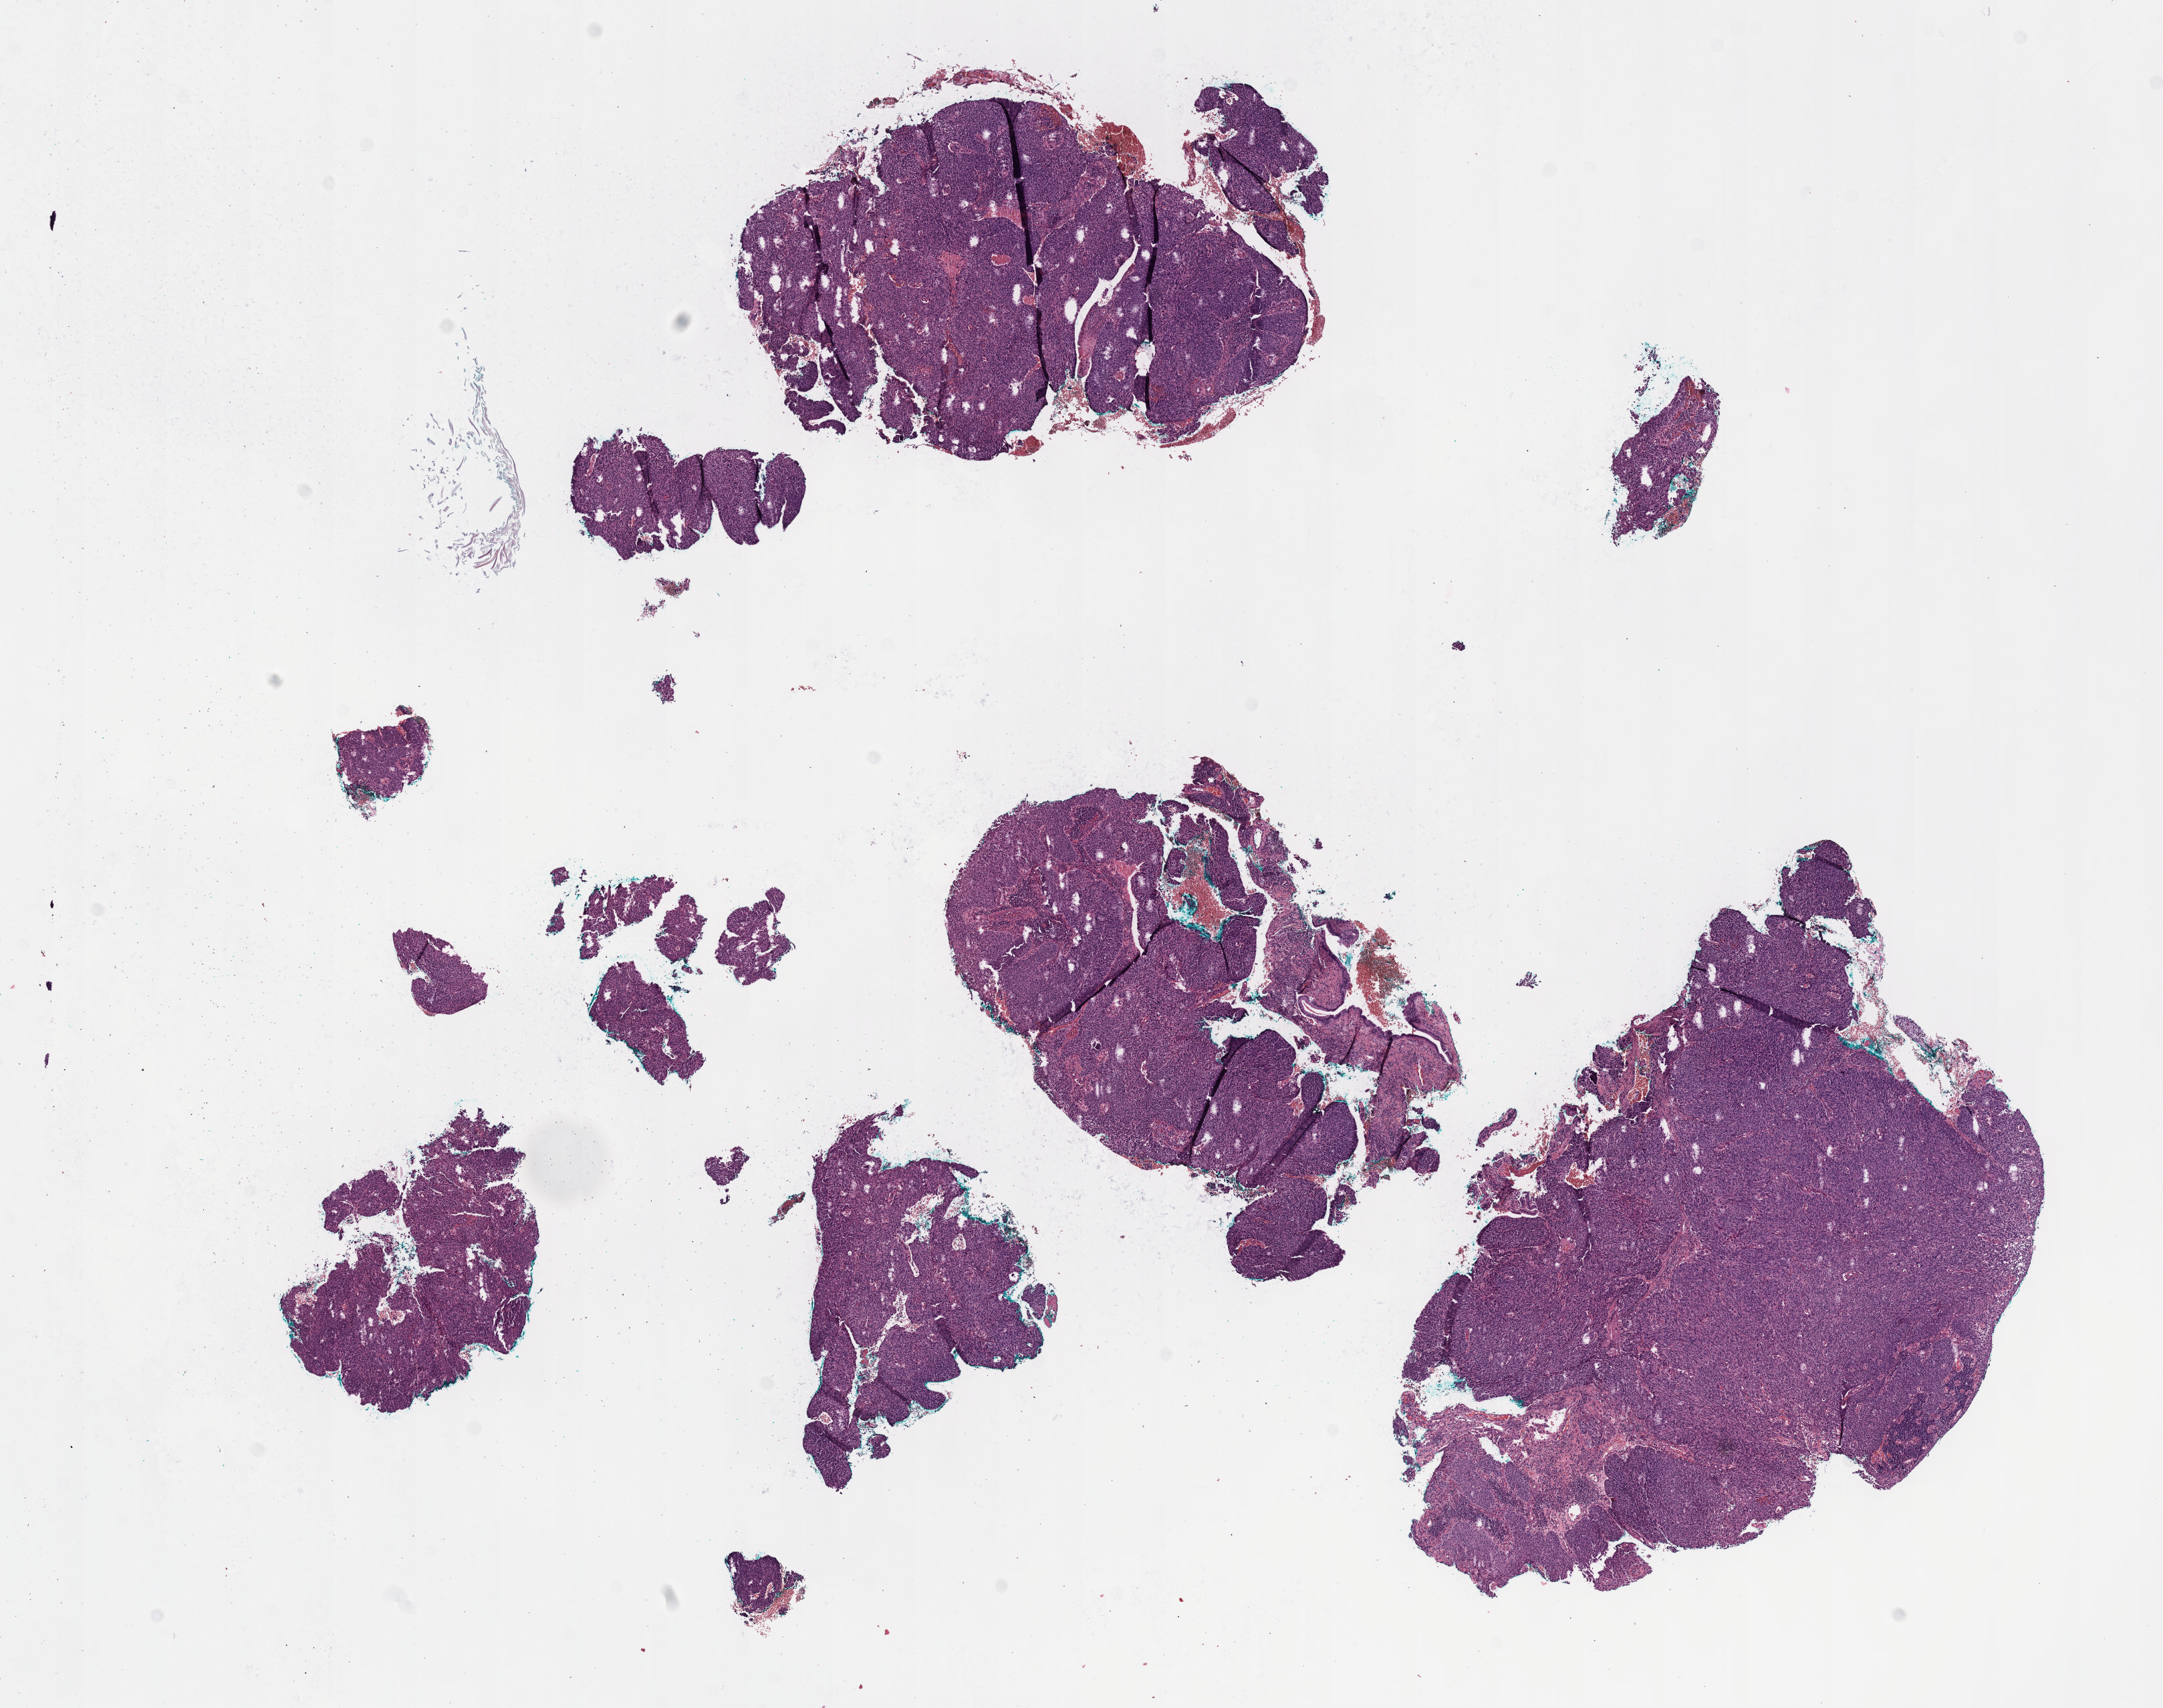
Whole-slide histology image, H&E, low-resolution overview of the scanned area, about 13.1 x 10.3 mm (from a 40x scan), formalin-fixed paraffin-embedded (FFPE) diagnostic section, cervix, primary tumour sample. Patient: female, age at initial diagnosis 30 years. Histologic grade: G3 (poorly differentiated).
* histologic diagnosis: Squamous cell carcinoma, NOS (cervix uteri)
* FIGO stage: IB1